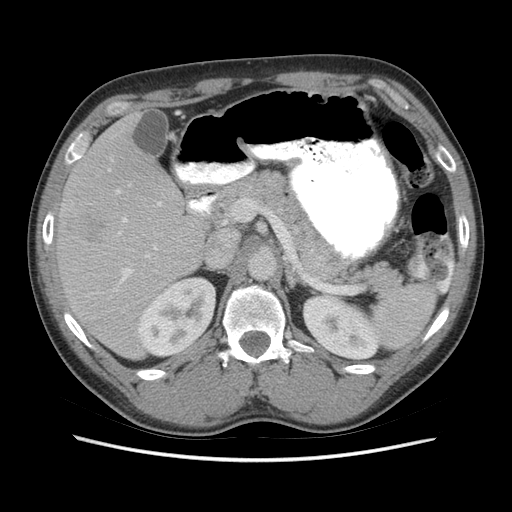
Contrast-enhanced abdominal CT (liver protocol), one axial slice; position 34 of 73 along the scan axis; 140 kVp; soft-tissue window (W 400 / L 40 HU); 2.5 mm slice thickness; 512 × 512 image matrix, field of view 360 × 360 mm. From the clinical record (not read from this slice): diagnosis: hepatocellular carcinoma (patient treated with transarterial chemoembolisation; whether this scan precedes or follows treatment is not stated here); TNM stage (as recorded): Stage-IIIA; Child-Pugh class: A; tumour size: 6.6 cm.
Annotated regions visible in this slice (semi-automatically segmented with operator editing):
- liver parenchyma outside the tumour (the mass and vessels are separate outlines, so this box may not span the whole liver): box from (x=54, y=112) to (x=210, y=358) px
- mass: (x=64, y=212)–(x=105, y=246)
- liver vessels: (x=108, y=168)–(x=161, y=282)